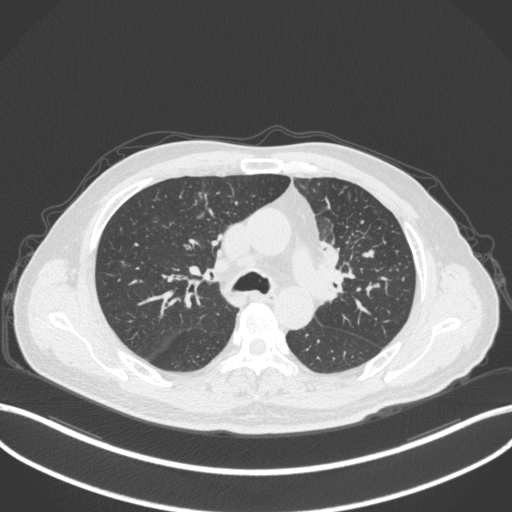
Chest CT, one axial slice; position 227 of 386 along the scan axis; reconstruction kernel B31f; 120 kVp; lung window (W 1500 / L -600 HU); 512 × 512 image matrix, field of view 400 × 400 mm. Patient: male, 69 years. Case-level facts recorded for this patient, not image findings: clinical TNM (as recorded): T2a N2 M0.
Outlined on this slice (bounding box drawn by a radiologist):
- lung tumour (recorded histology: adenocarcinoma): bounding box <318,241,350,293> (left, top, right, bottom; pixels)